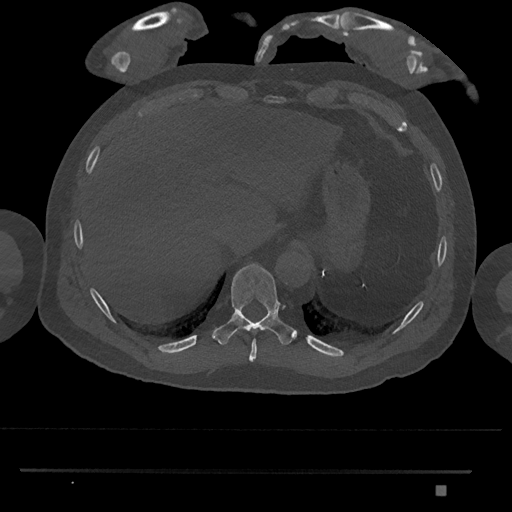
CT including the spine, one axial slice. Slice 1008 of 1134 in the series (ordered by position). Bone window (W 1800 / L 400 HU). 0.5 mm slice thickness. 512 × 512 image matrix. Male patient, age 65 years. From the clinical record (not read from this slice): primary cancer: prostate.
Annotated regions visible in this slice (semi-automatic segmentation, software-assisted and operator-edited):
- T10 vertebra: bounding box (x1, y1, x2, y2) in pixels: (212, 264, 296, 345)
- T9 vertebra: (249, 339, 257, 362)